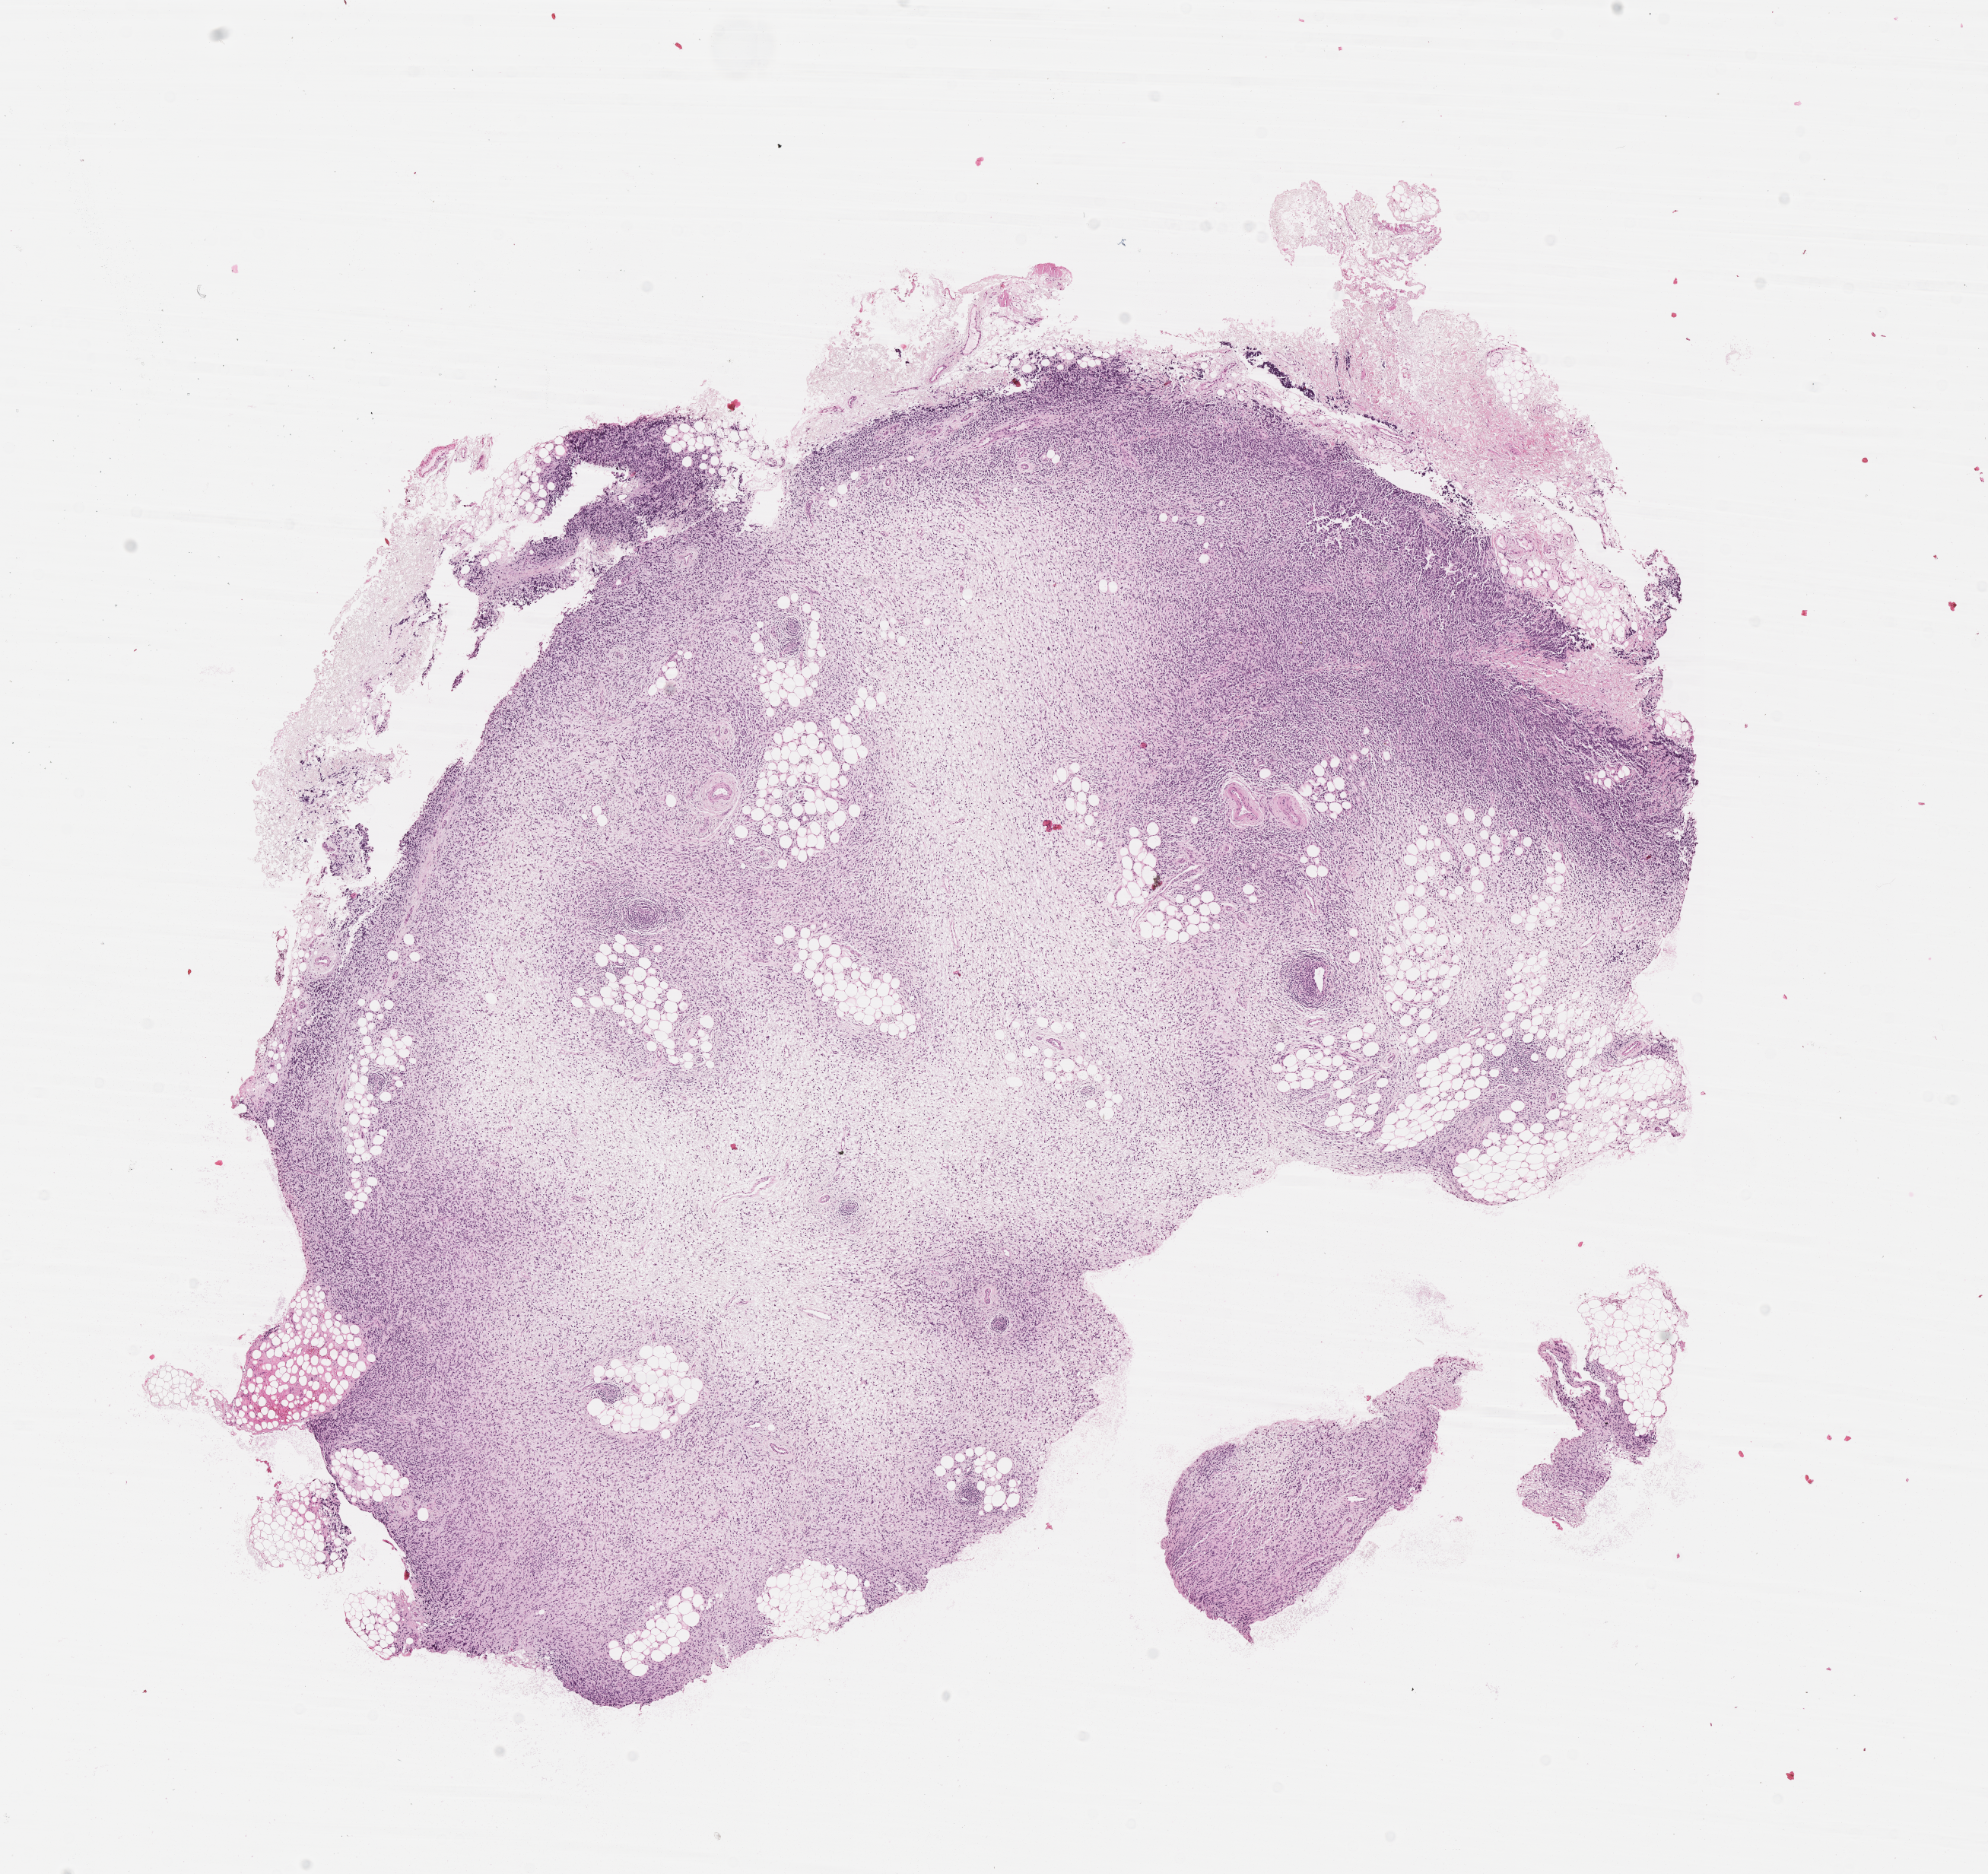
Digitized haematoxylin and eosin-stained section of tumor tissue — shown as a low-resolution overview of the whole scanned area (about 10.6 x 10.0 mm); formalin-fixed paraffin-embedded section; sample anatomic site: eye - orbit, right. Patient: male, age 4.3 years at diagnosis.
Stage (as recorded): 1. Metastatic status at presentation (as recorded): non-metastatic (confirmed). Diagnosis: rhabdomyosarcoma; histological classification: embryonal rhabdomyosarcoma.